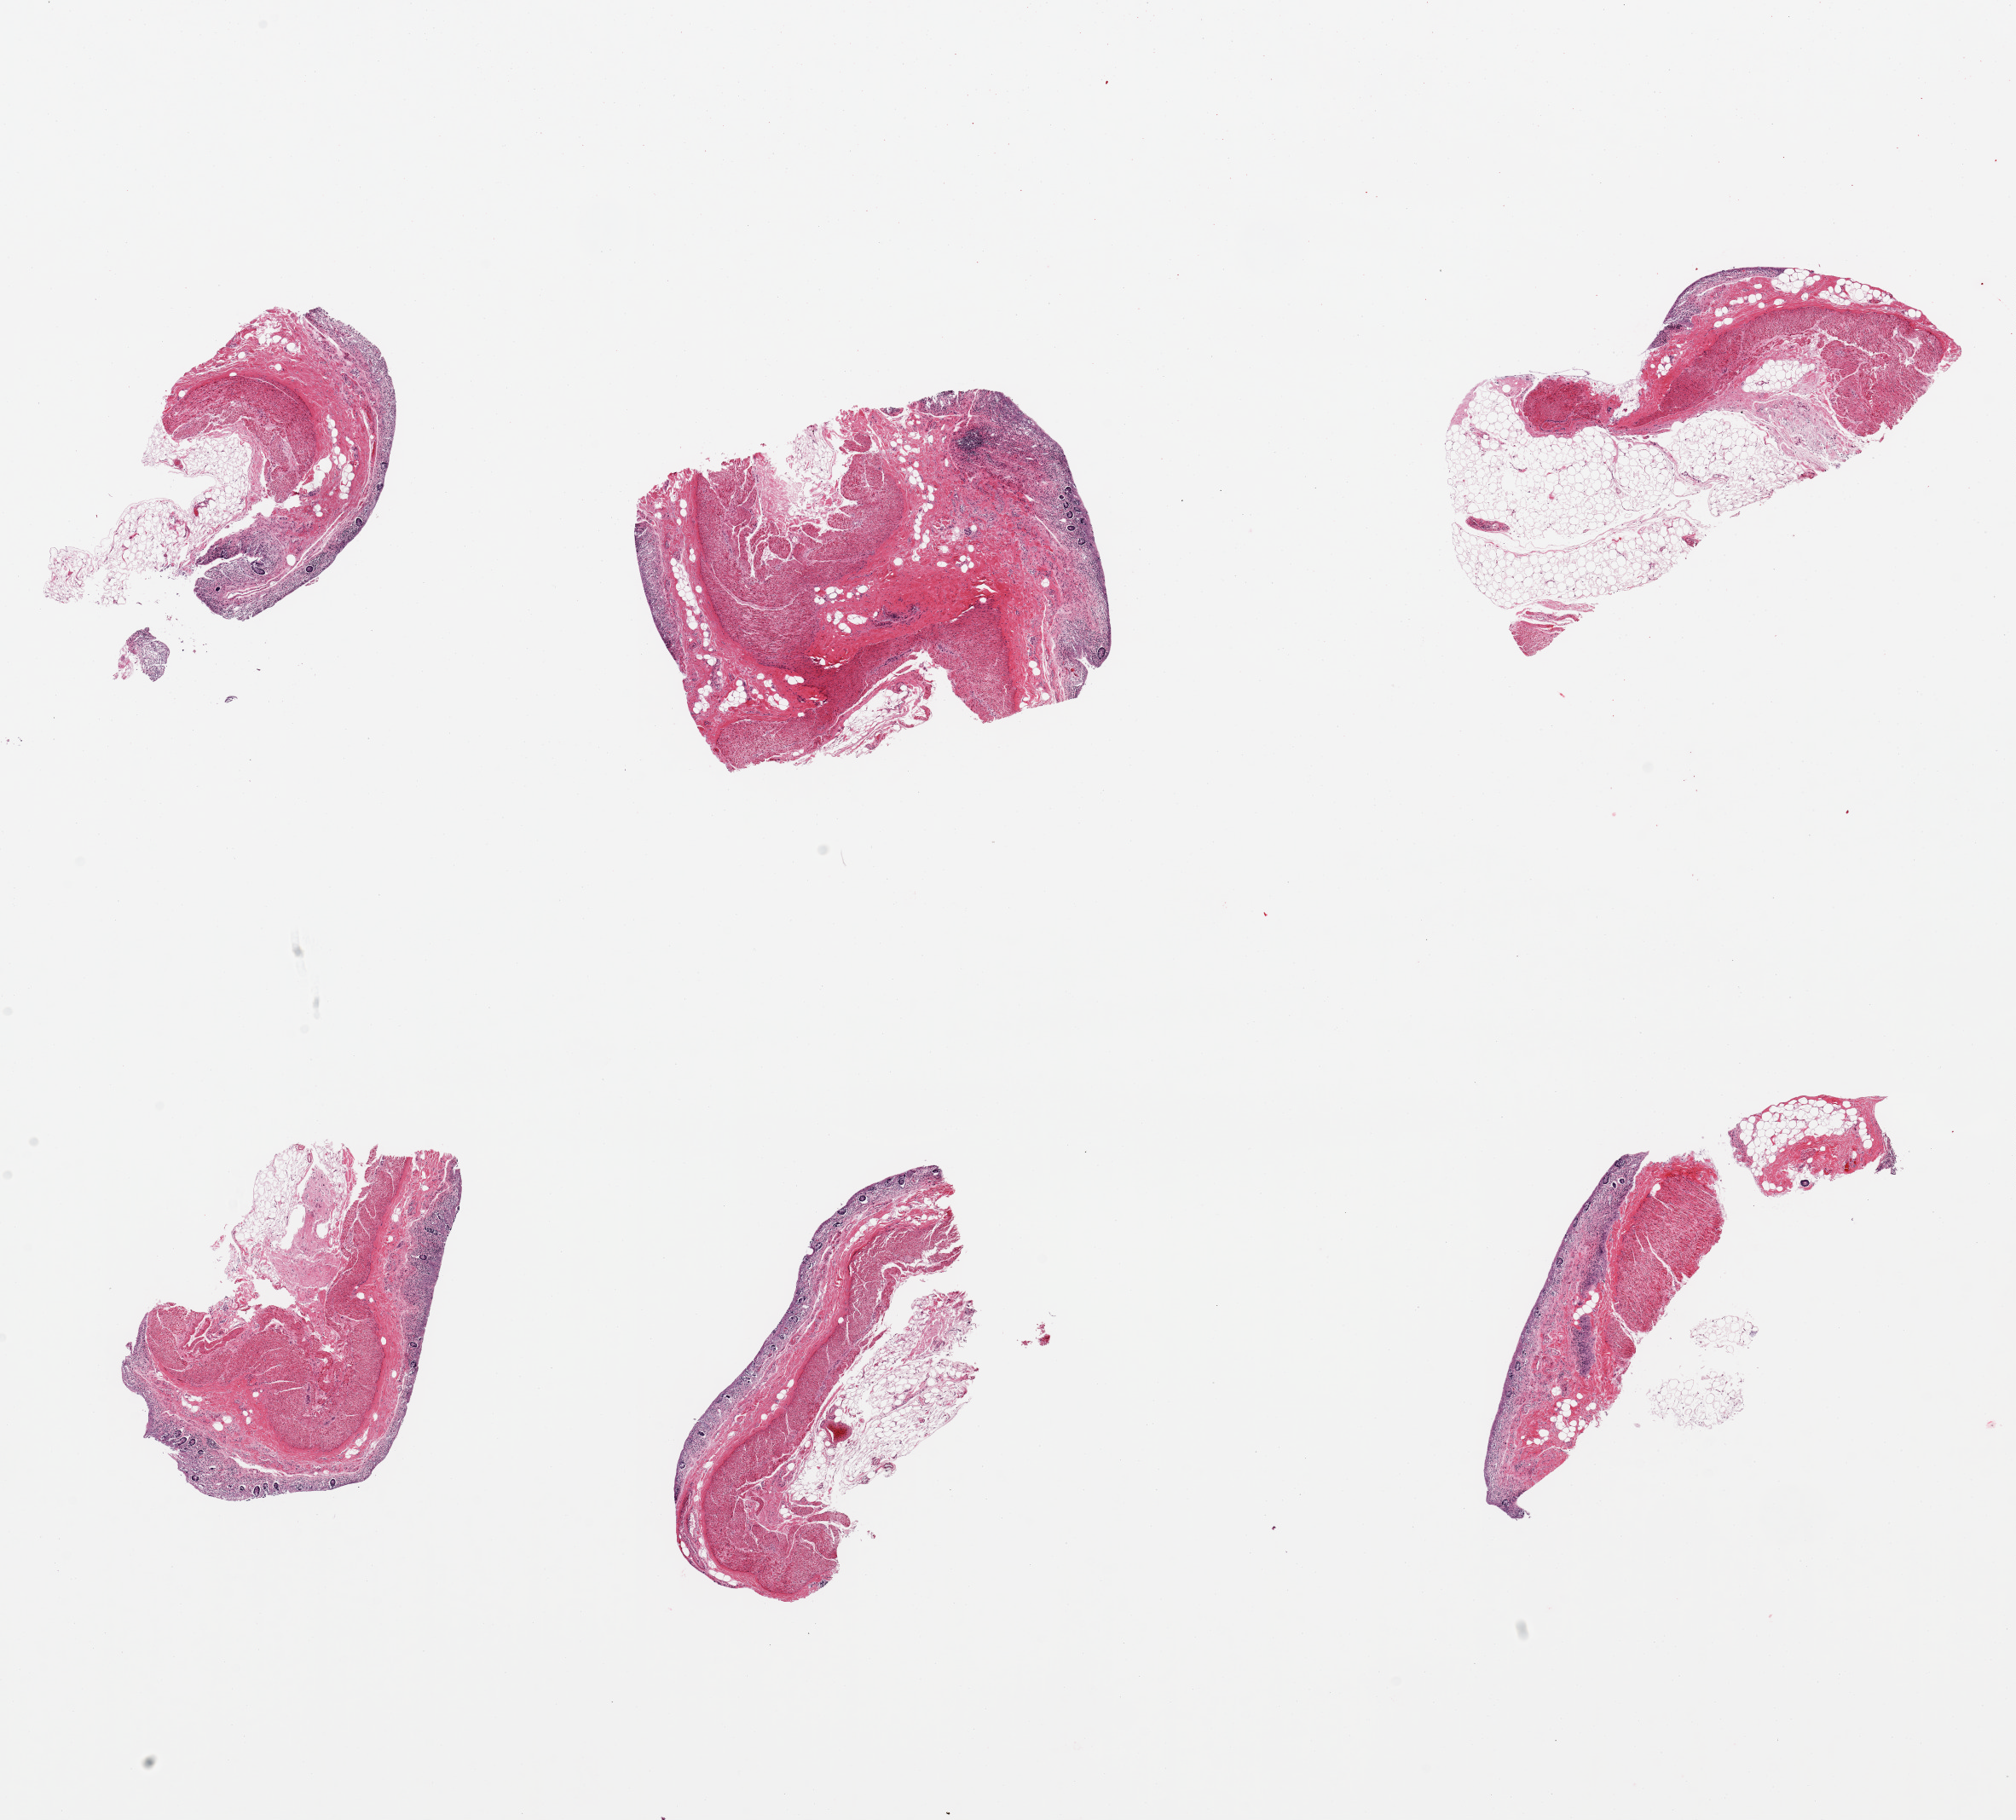
Whole-slide image, H&E stain — shown as a low-resolution overview of the whole scanned area (about 18.7 x 16.9 mm). Donor sex: male.
Specimen: PAXgene-fixed, paraffin-embedded tissue; sampled site (target tissue): transverse colon; donor tissue sample.